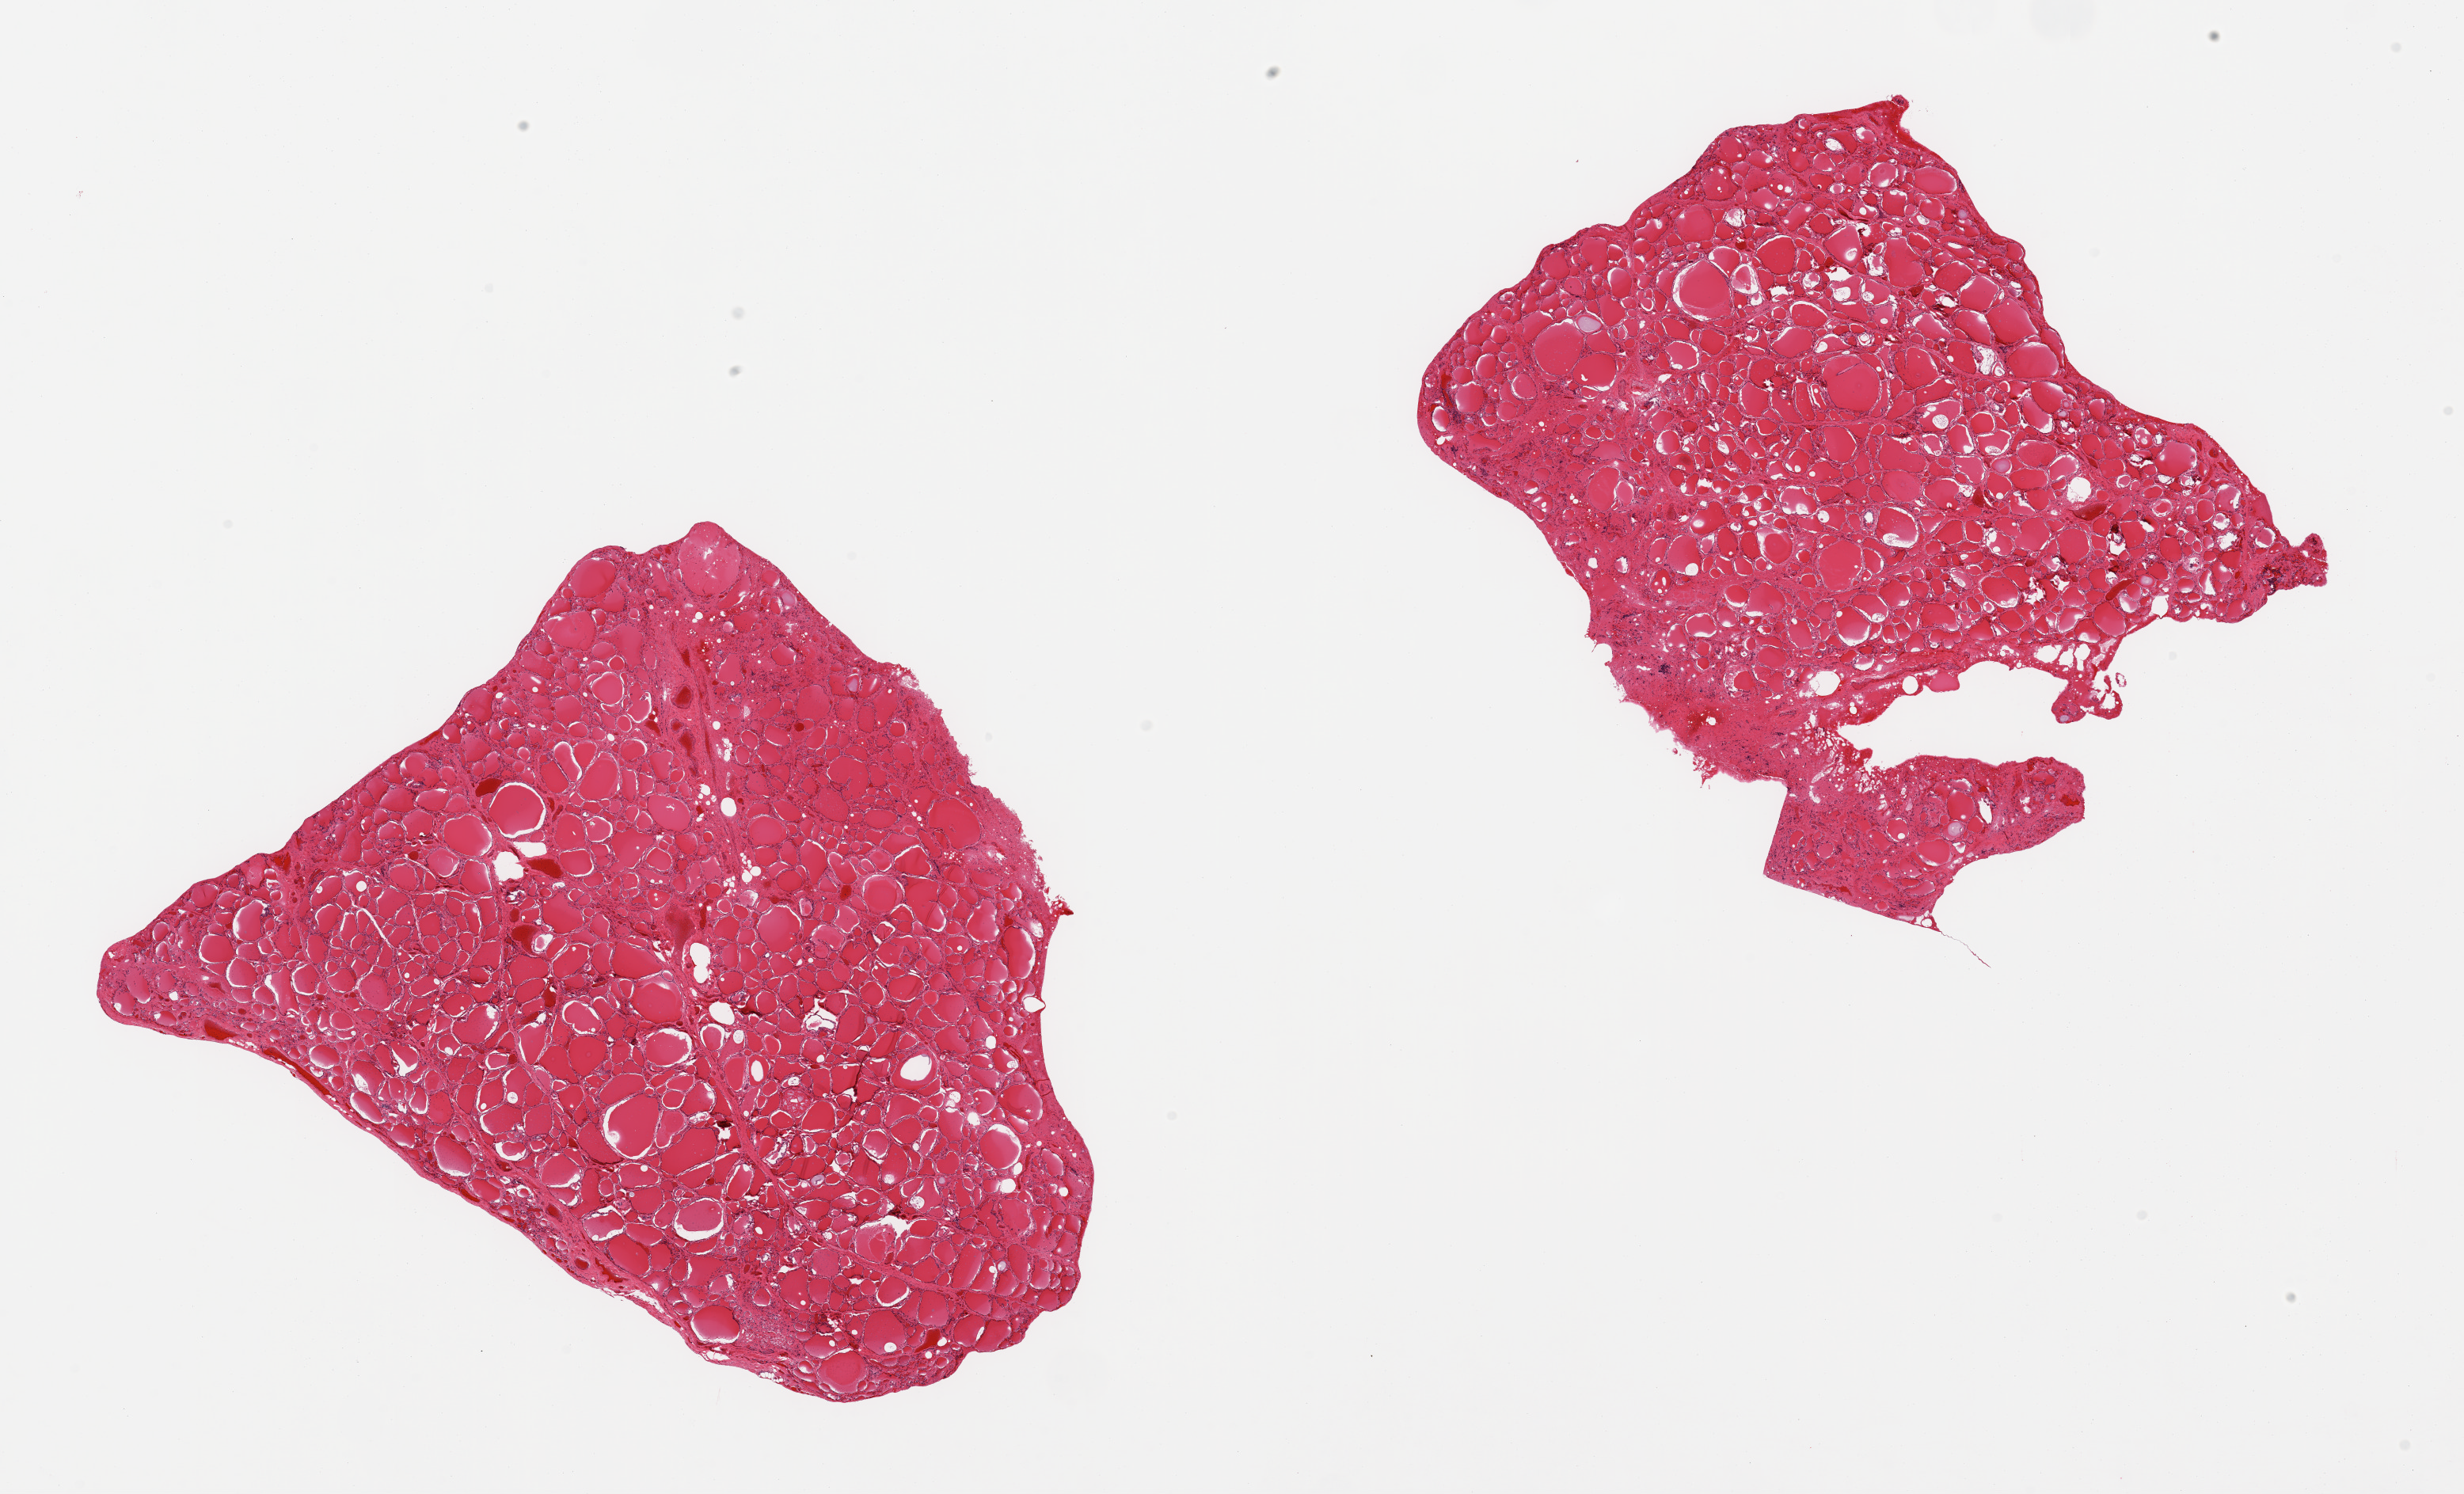
Digitized hematoxylin and eosin (H&E)-stained section, whole scanned area (about 24.6 x 14.9 mm, slide scanned at 20x) shown as a low-resolution overview. PAXgene-fixed paraffin-embedded (PFPE) section. Sampled site (target tissue): thyroid. Tissue donor sample.
* reviewer comment on this tissue sample: 2 pieces, no significant abnormalities